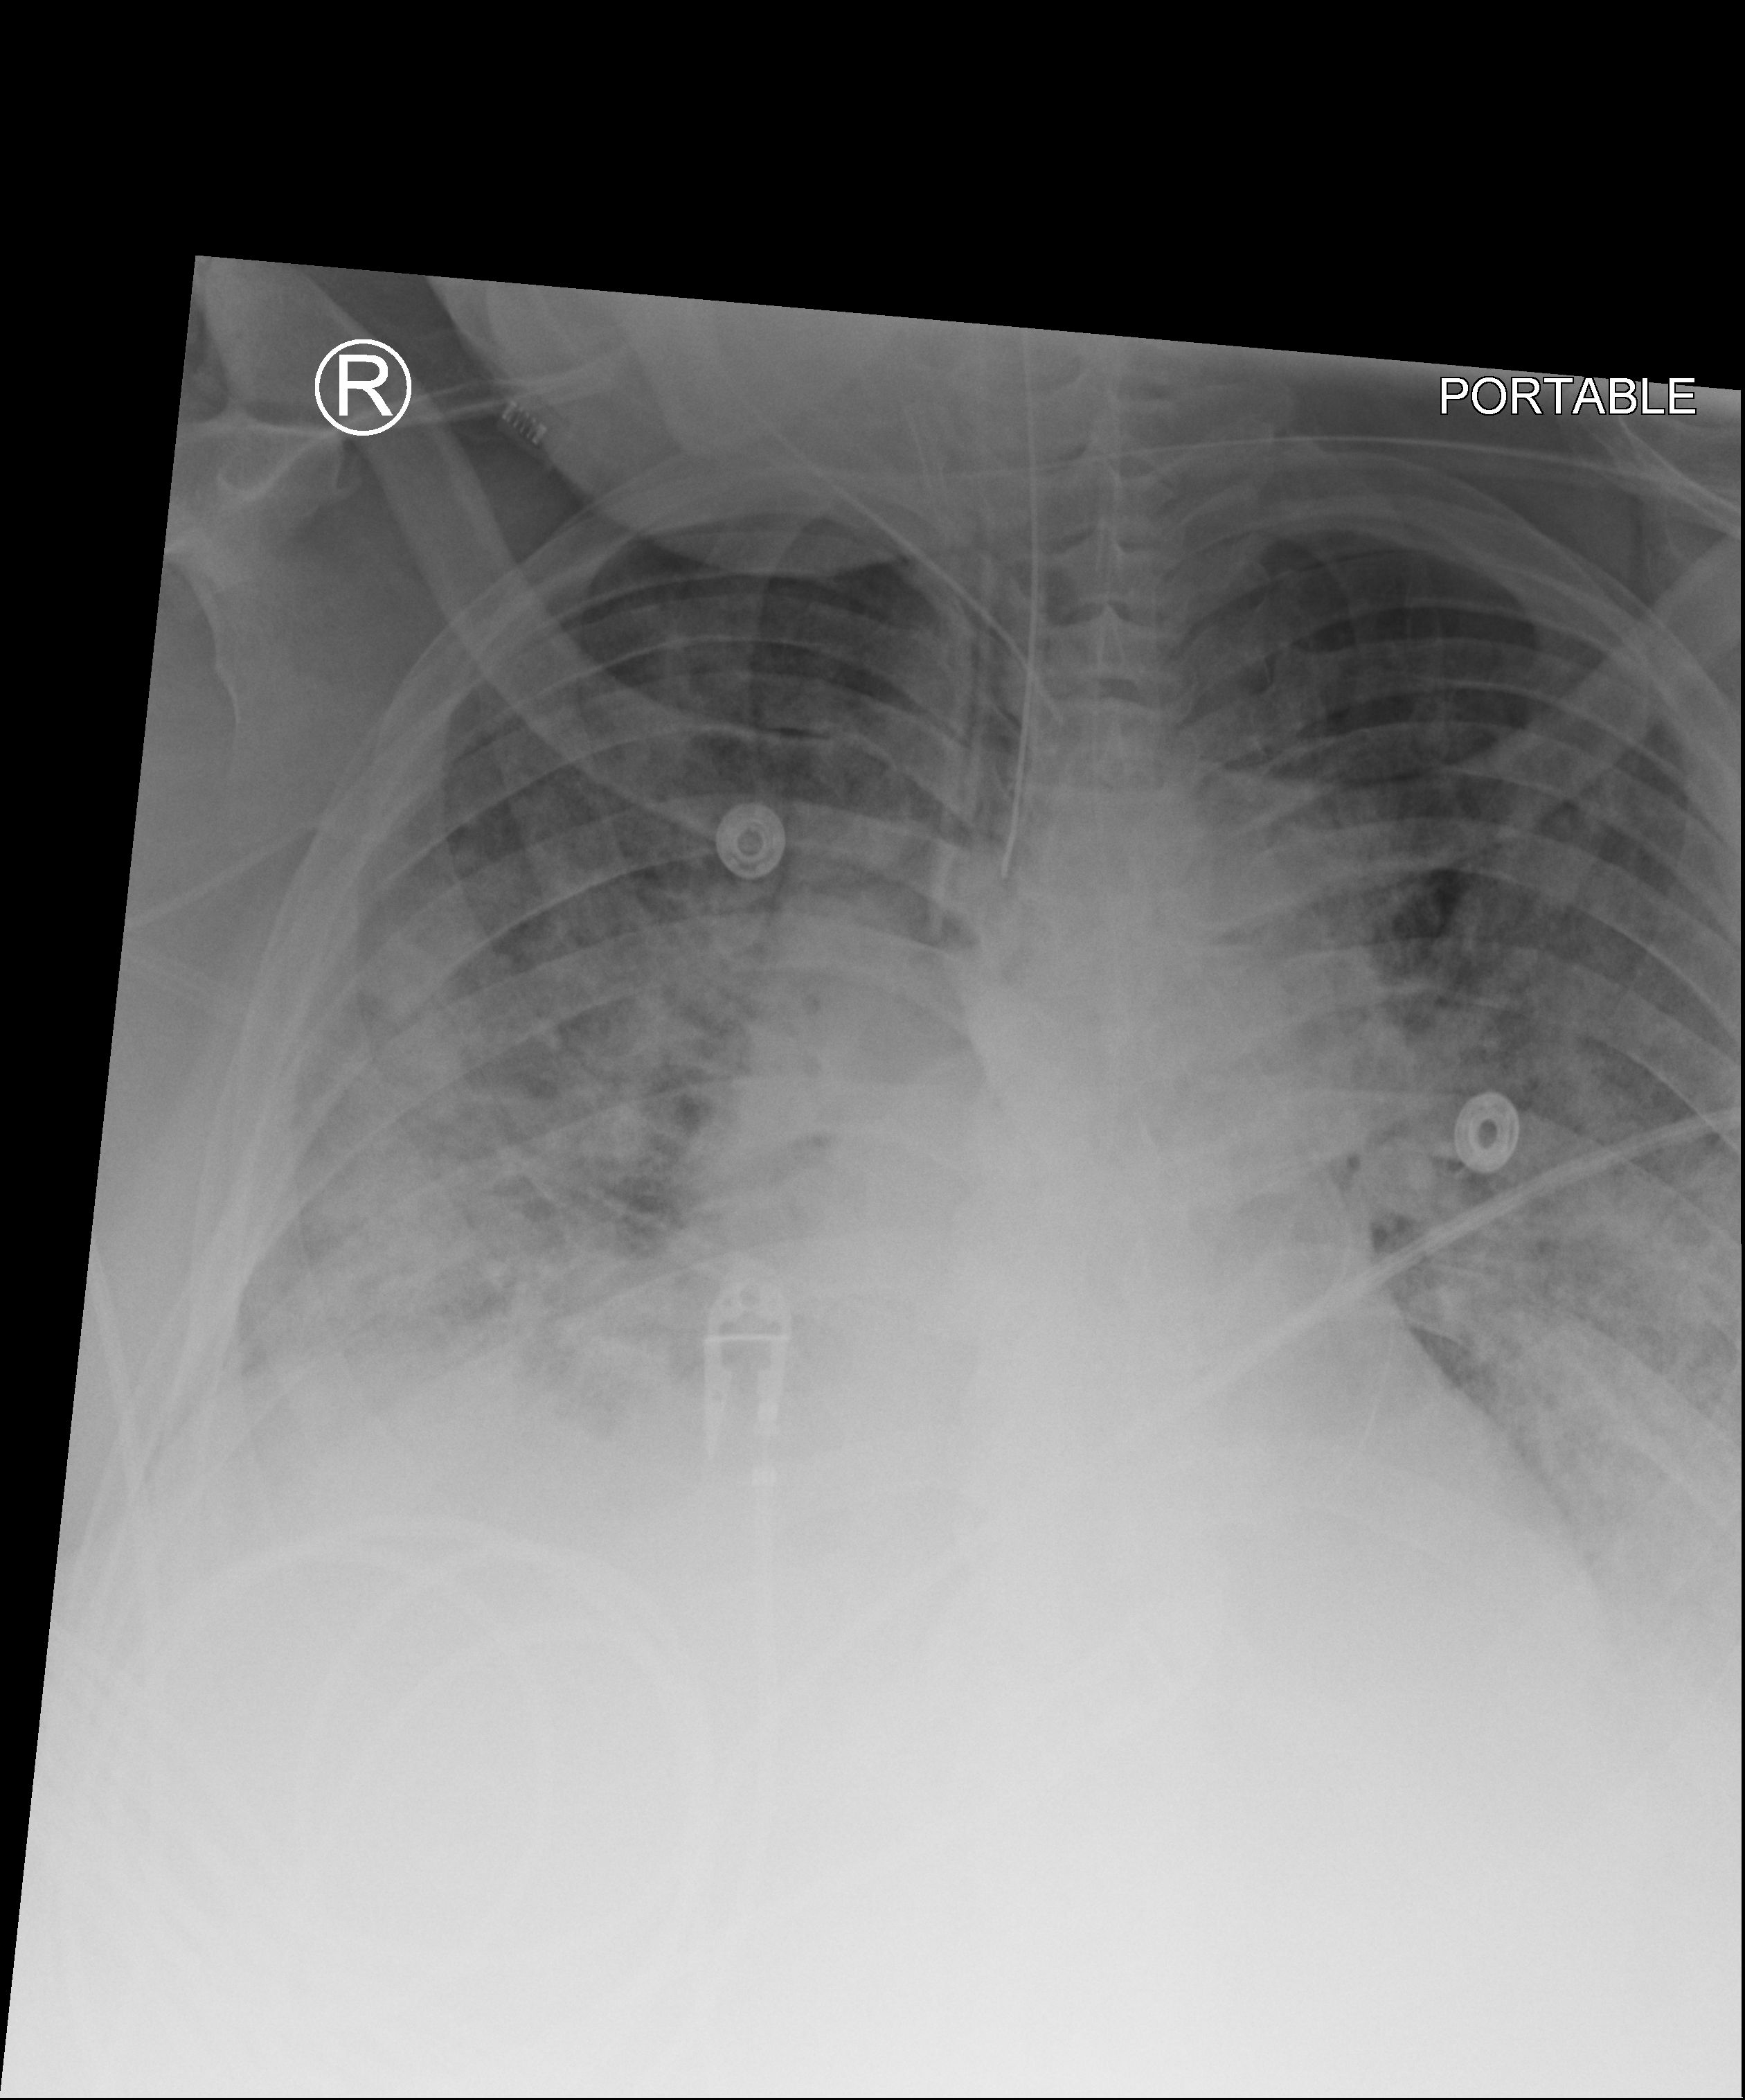
Portable chest radiograph, anteroposterior (AP) projection. Patient hospitalised with COVID-19; male, aged 60–74 years.
Hospital-stay facts (about this admission, not read from this image; timing relative to this image not recorded): COPD (admission record): no.